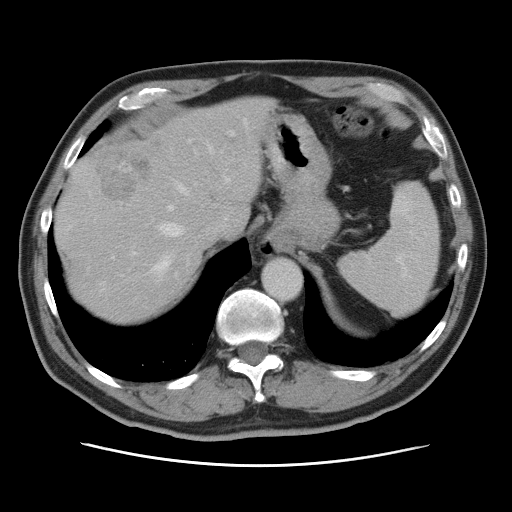
Contrast-enhanced abdominal CT, one axial slice; slice 61 of 80 in the series (ordered by position); soft-tissue window (W 400 / L 40 HU); 512 × 512 image matrix, field of view 370 × 370 mm. Male patient, age 69 years. Case-level facts recorded for this patient, not image findings: diagnosis: colorectal cancer liver metastases, imaged before liver resection; multiple liver metastases: no; largest metastasis: 5 cm; disease in both lobes: yes.
Annotated regions visible in this slice (manually delineated by an expert):
- hepatic veins: box from (x=151, y=125) to (x=247, y=277) px
- liver: (x=56, y=97)–(x=271, y=327)
- planned liver remnant (the part of the liver to remain after resection): (x=56, y=97)–(x=272, y=327)
- portal vein (with intrahepatic branches): (x=130, y=130)–(x=234, y=275)
- liver metastasis: (x=93, y=151)–(x=151, y=201)